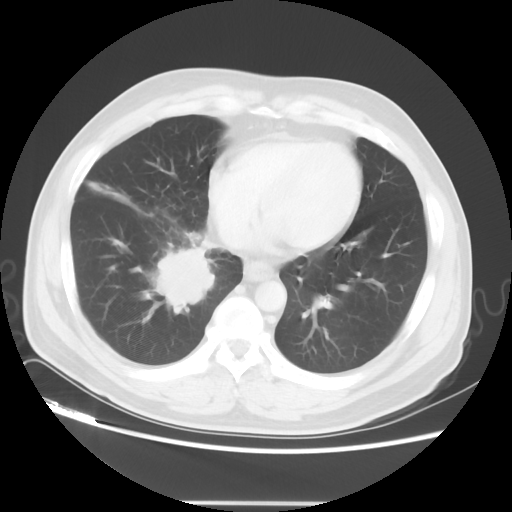
Chest CT, one axial slice. Position 16 of 48 along the scan axis. Reconstruction kernel STANDARD. Lung window (W 1500 / L -600 HU). 512 × 512 image matrix, field of view 390 × 390 mm. Patient: male, 53 years. Case-level facts recorded for this patient, not image findings: clinical TNM (as recorded): T2 N3 M0; histopathological grade: G3.
Annotated regions visible in this slice (rectangle marked by the reading radiologist):
- lung tumour (recorded histology: small cell carcinoma): box from (x=155, y=242) to (x=216, y=318) px